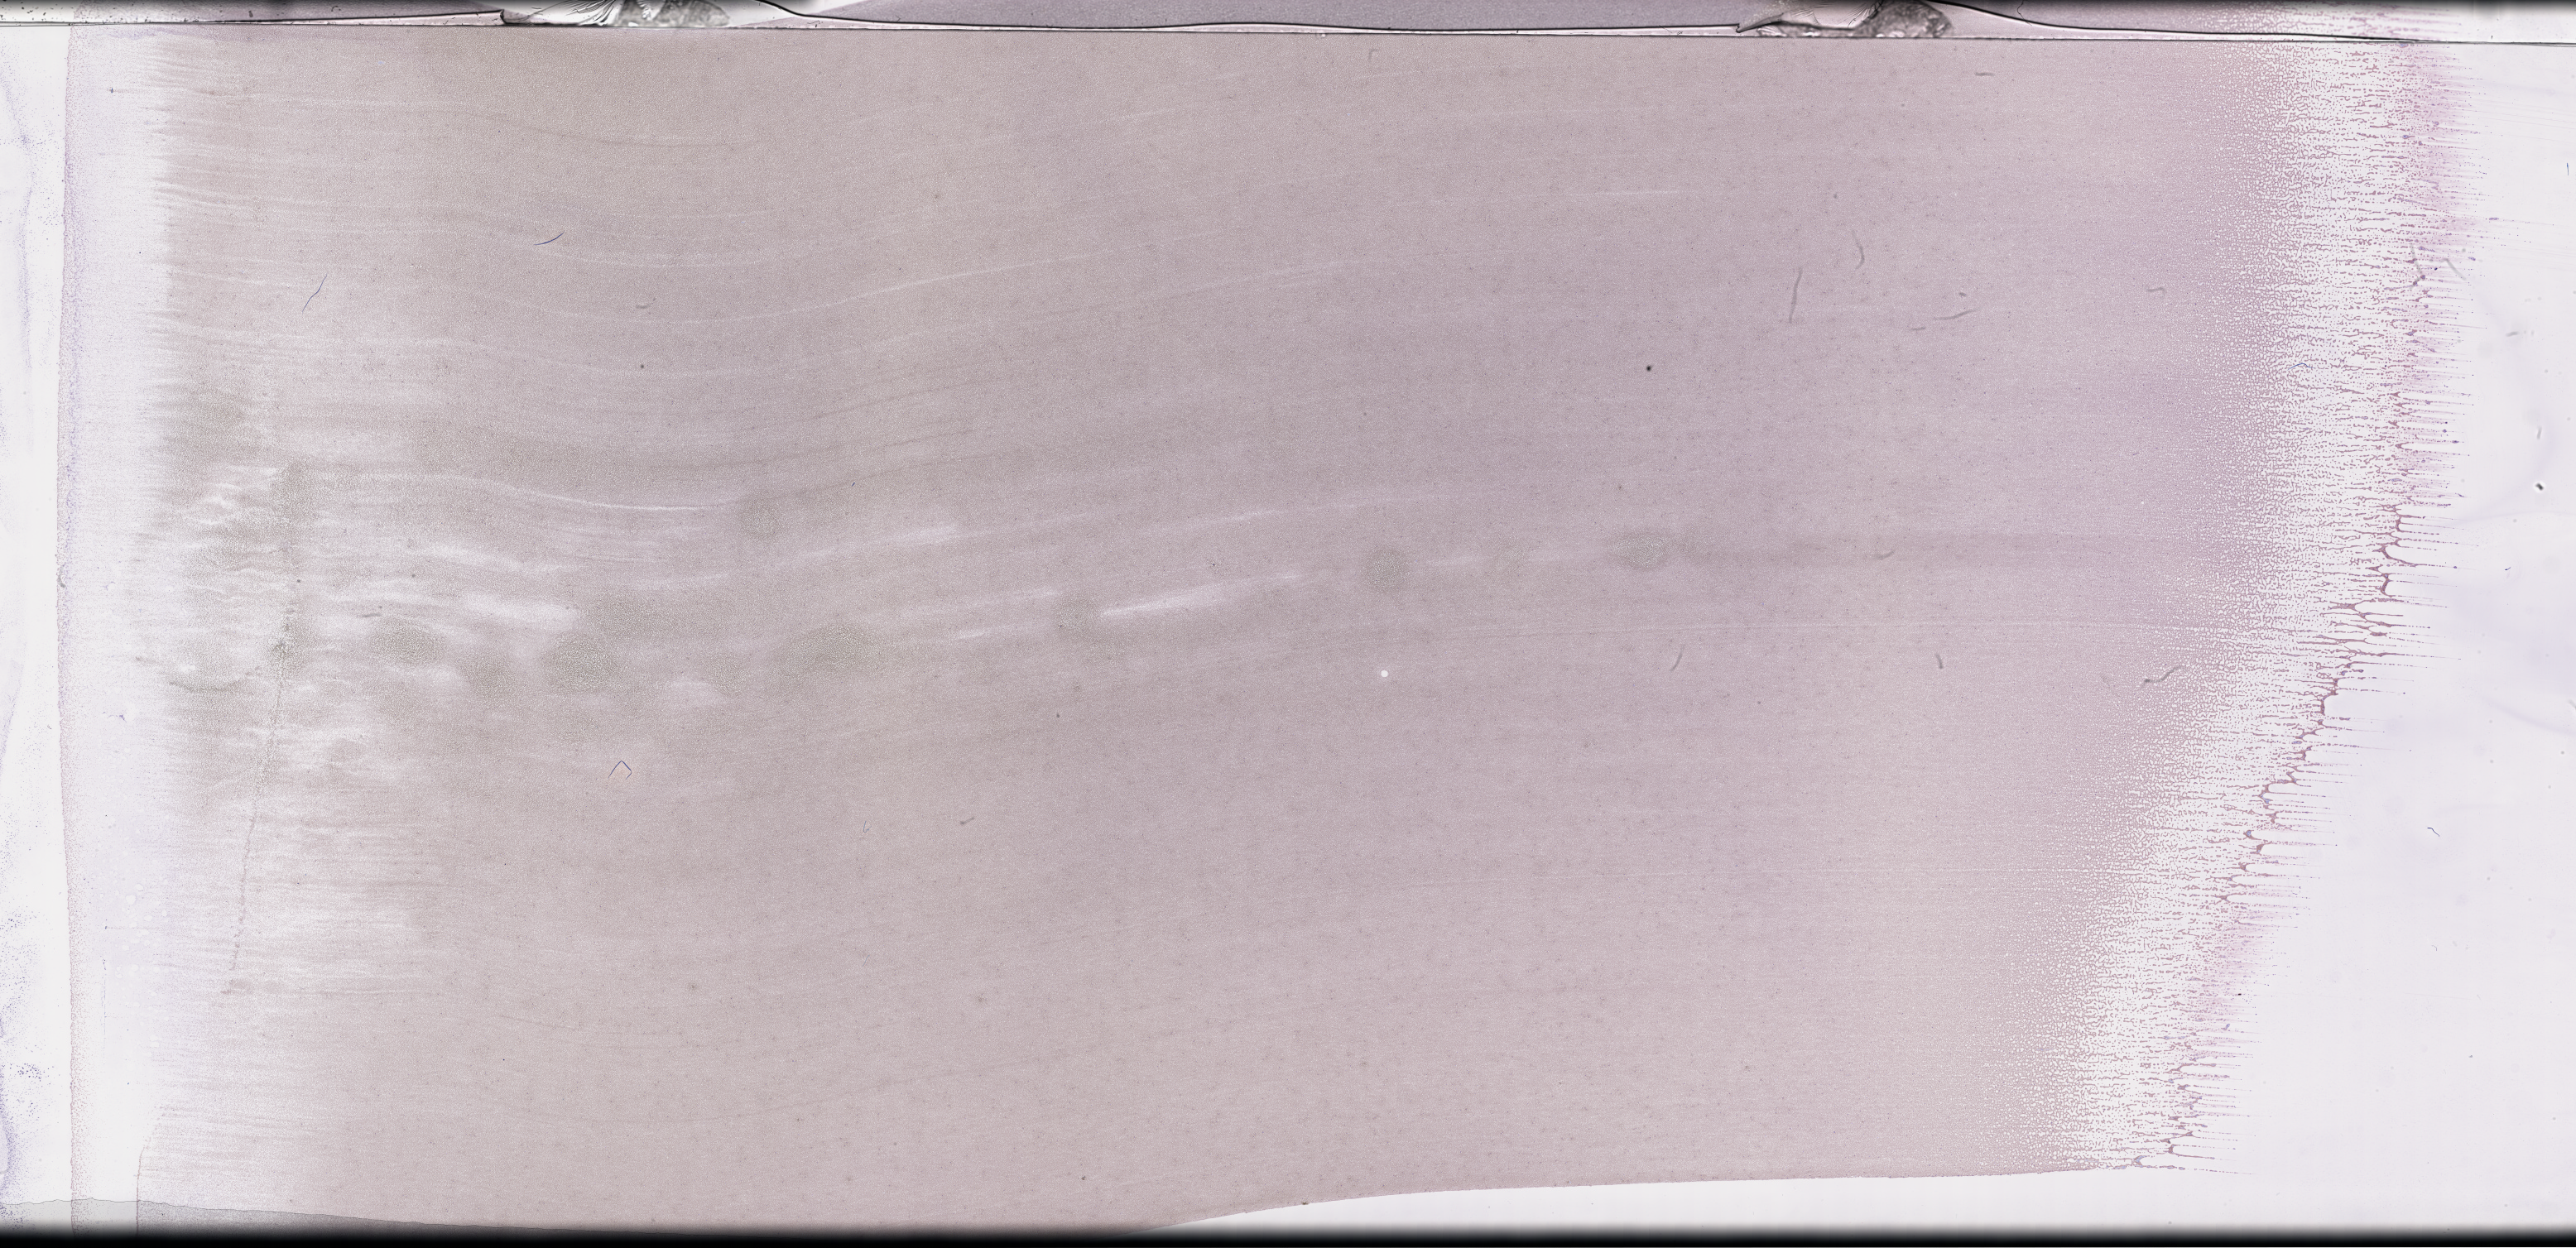
Wright–Giemsa-stained whole blood smear, whole-slide image, shown as a low-resolution overview of the whole scanned area (about 50.3 x 24.4 mm). EDTA-anticoagulated smear. Patient: female.
Patient diagnosis: Plasma Cell Myeloma.